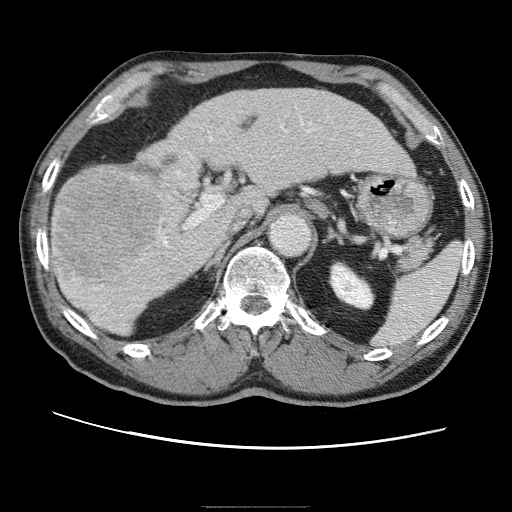
Contrast-enhanced abdominal CT (liver protocol), one axial slice. Slice 32 of 75 in the series (ordered by position). One of 2 acquisitions stored at this slice position. Soft-tissue window (W 400 / L 40 HU). 2.5 mm slice thickness. 512 × 512 image matrix. From the clinical record (not read from this slice): diagnosis: hepatocellular carcinoma (patient treated with transarterial chemoembolisation; whether this scan precedes or follows treatment is not stated here); TNM stage (as recorded): Stage-II; Child-Pugh class: A; tumour size: 2 cm.
Outlined on this slice (semi-automatic segmentation, software-assisted and operator-edited):
- liver parenchyma outside the tumour (the mass and vessels are separate outlines, so this box may not span the whole liver): bounding box <52,90,408,330> (left, top, right, bottom; pixels)
- mass: <54,170,162,286>
- liver vessels: <93,120,344,302>